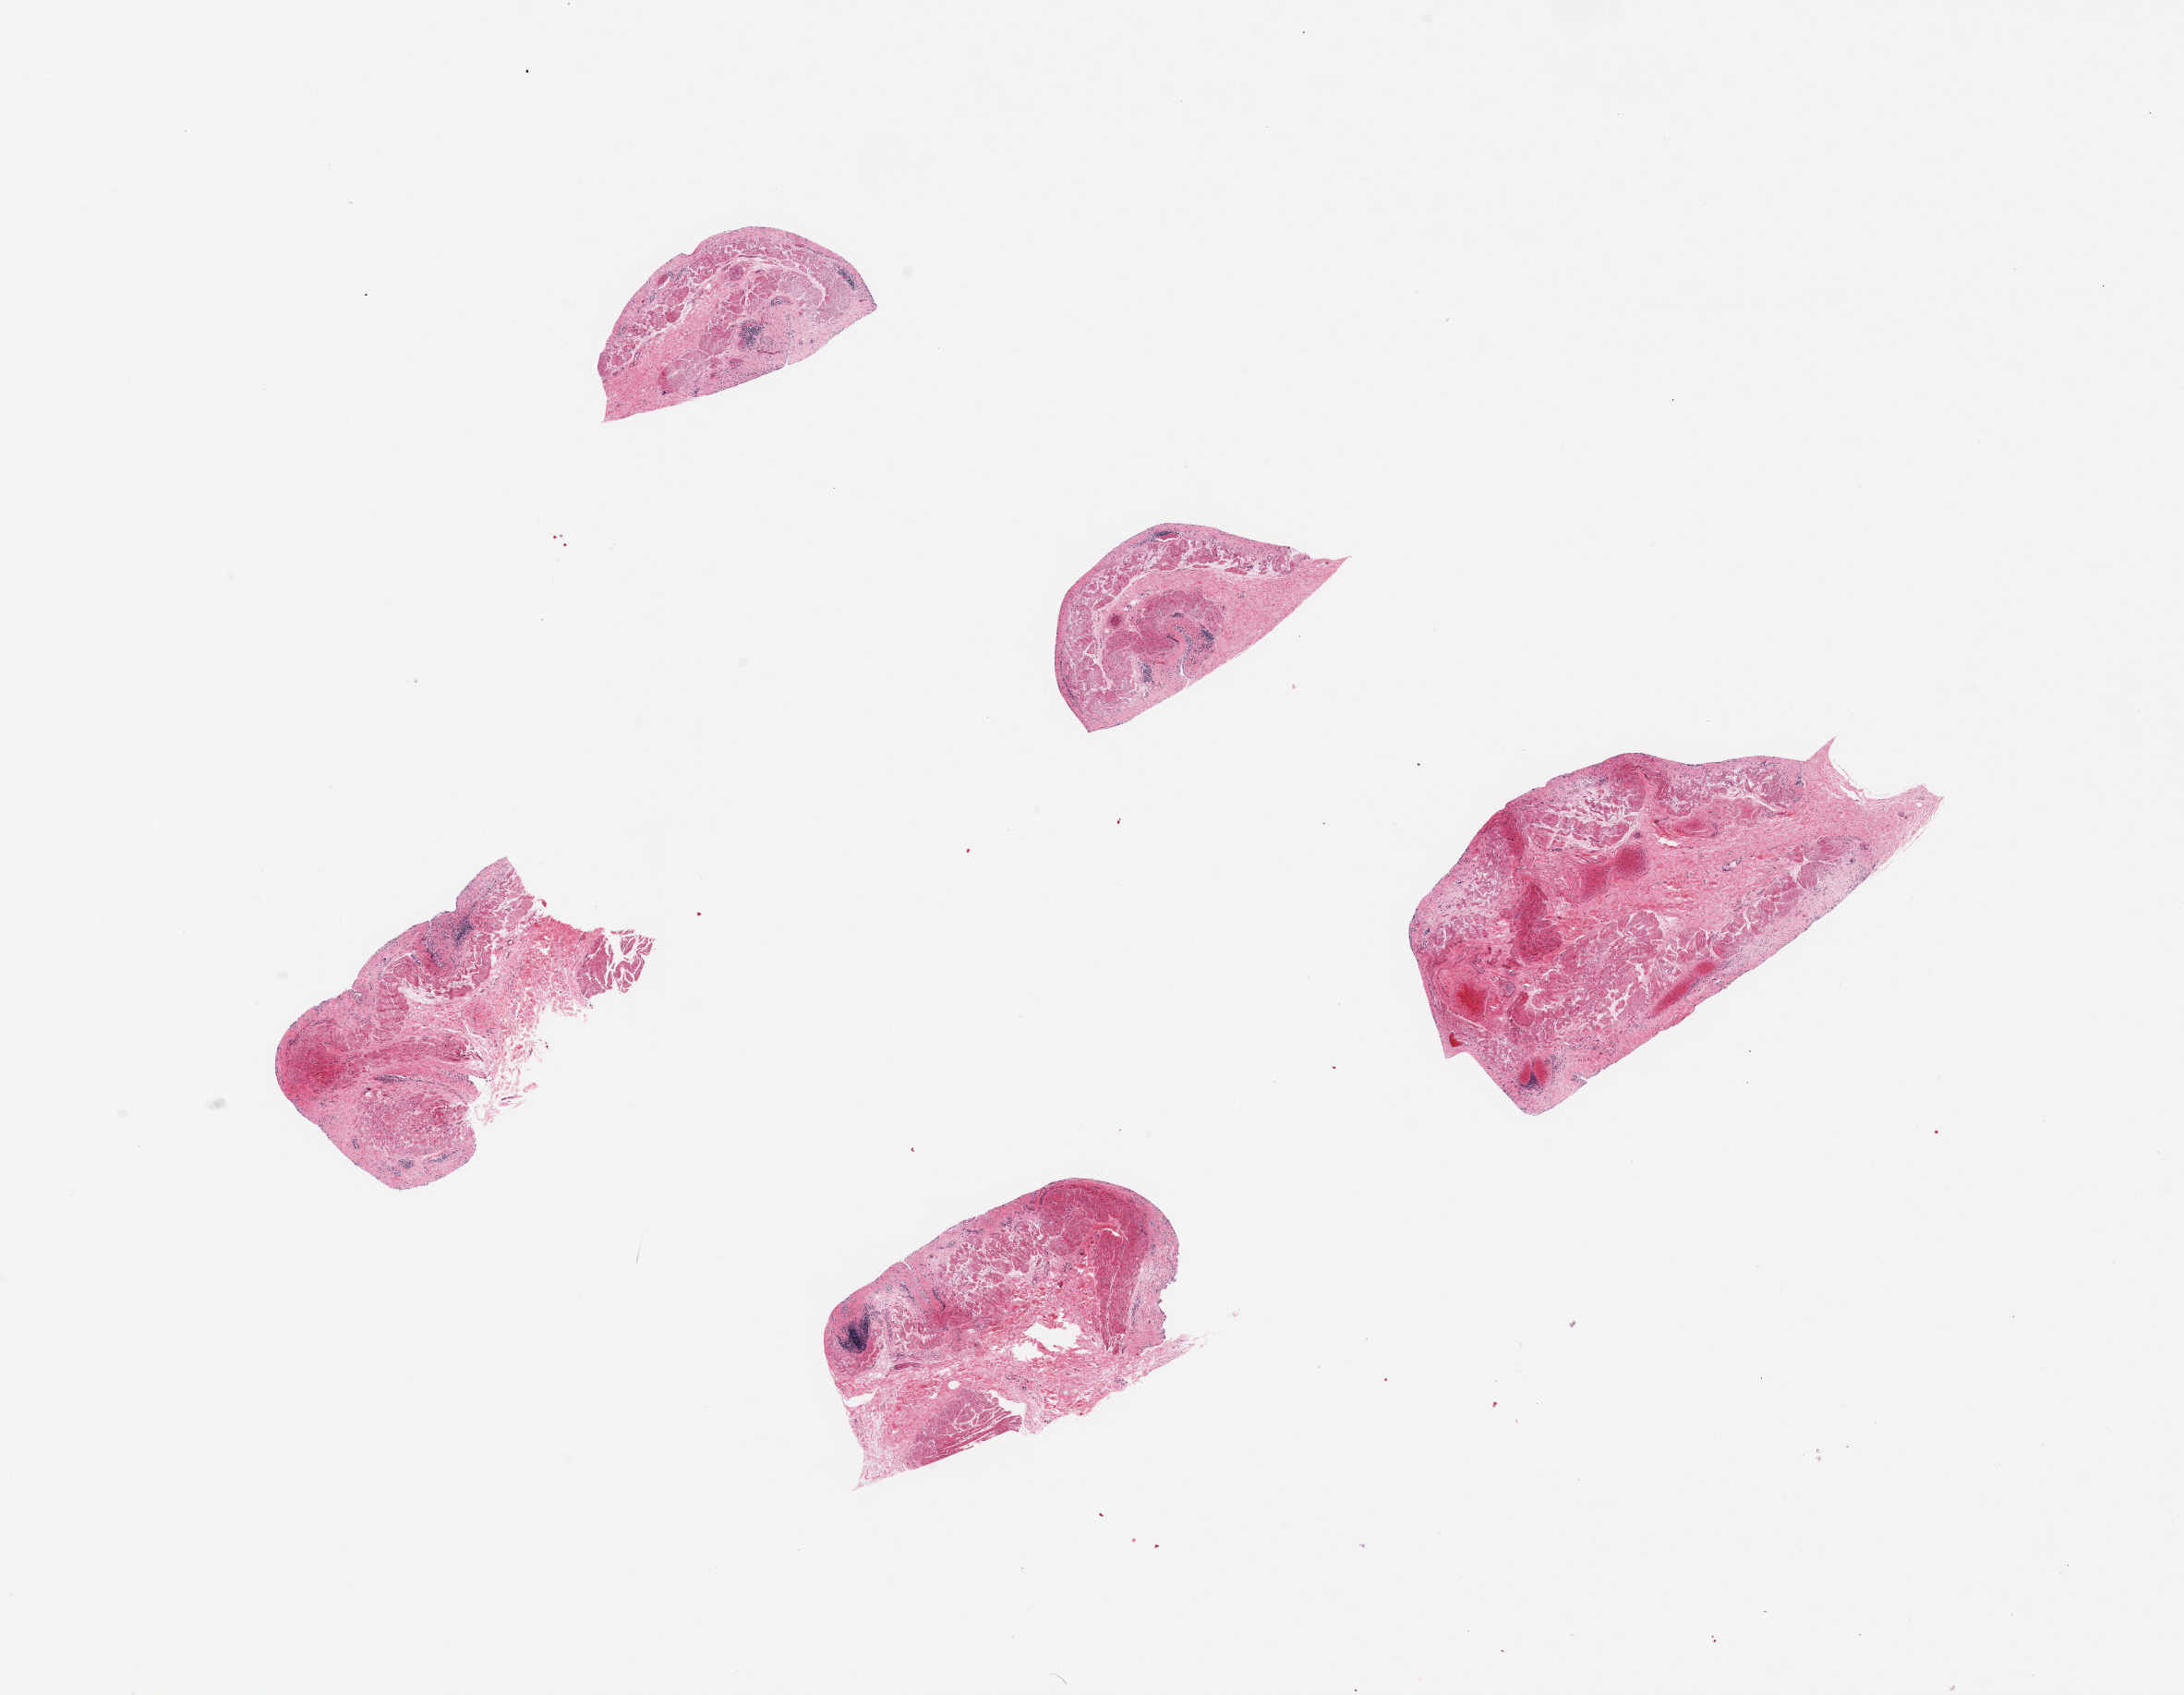
Digitized hematoxylin and eosin (H&E)-stained section — a low-resolution overview of the entire scanned area, about 18.7 x 14.5 mm, PAXgene-fixed, paraffin-embedded tissue, section of esophageal mucous membrane (target tissue), donor tissue sample. Male donor.
* review note (as recorded): 5 pieces; no epithelial layer, only muscularis mucosae & stroma